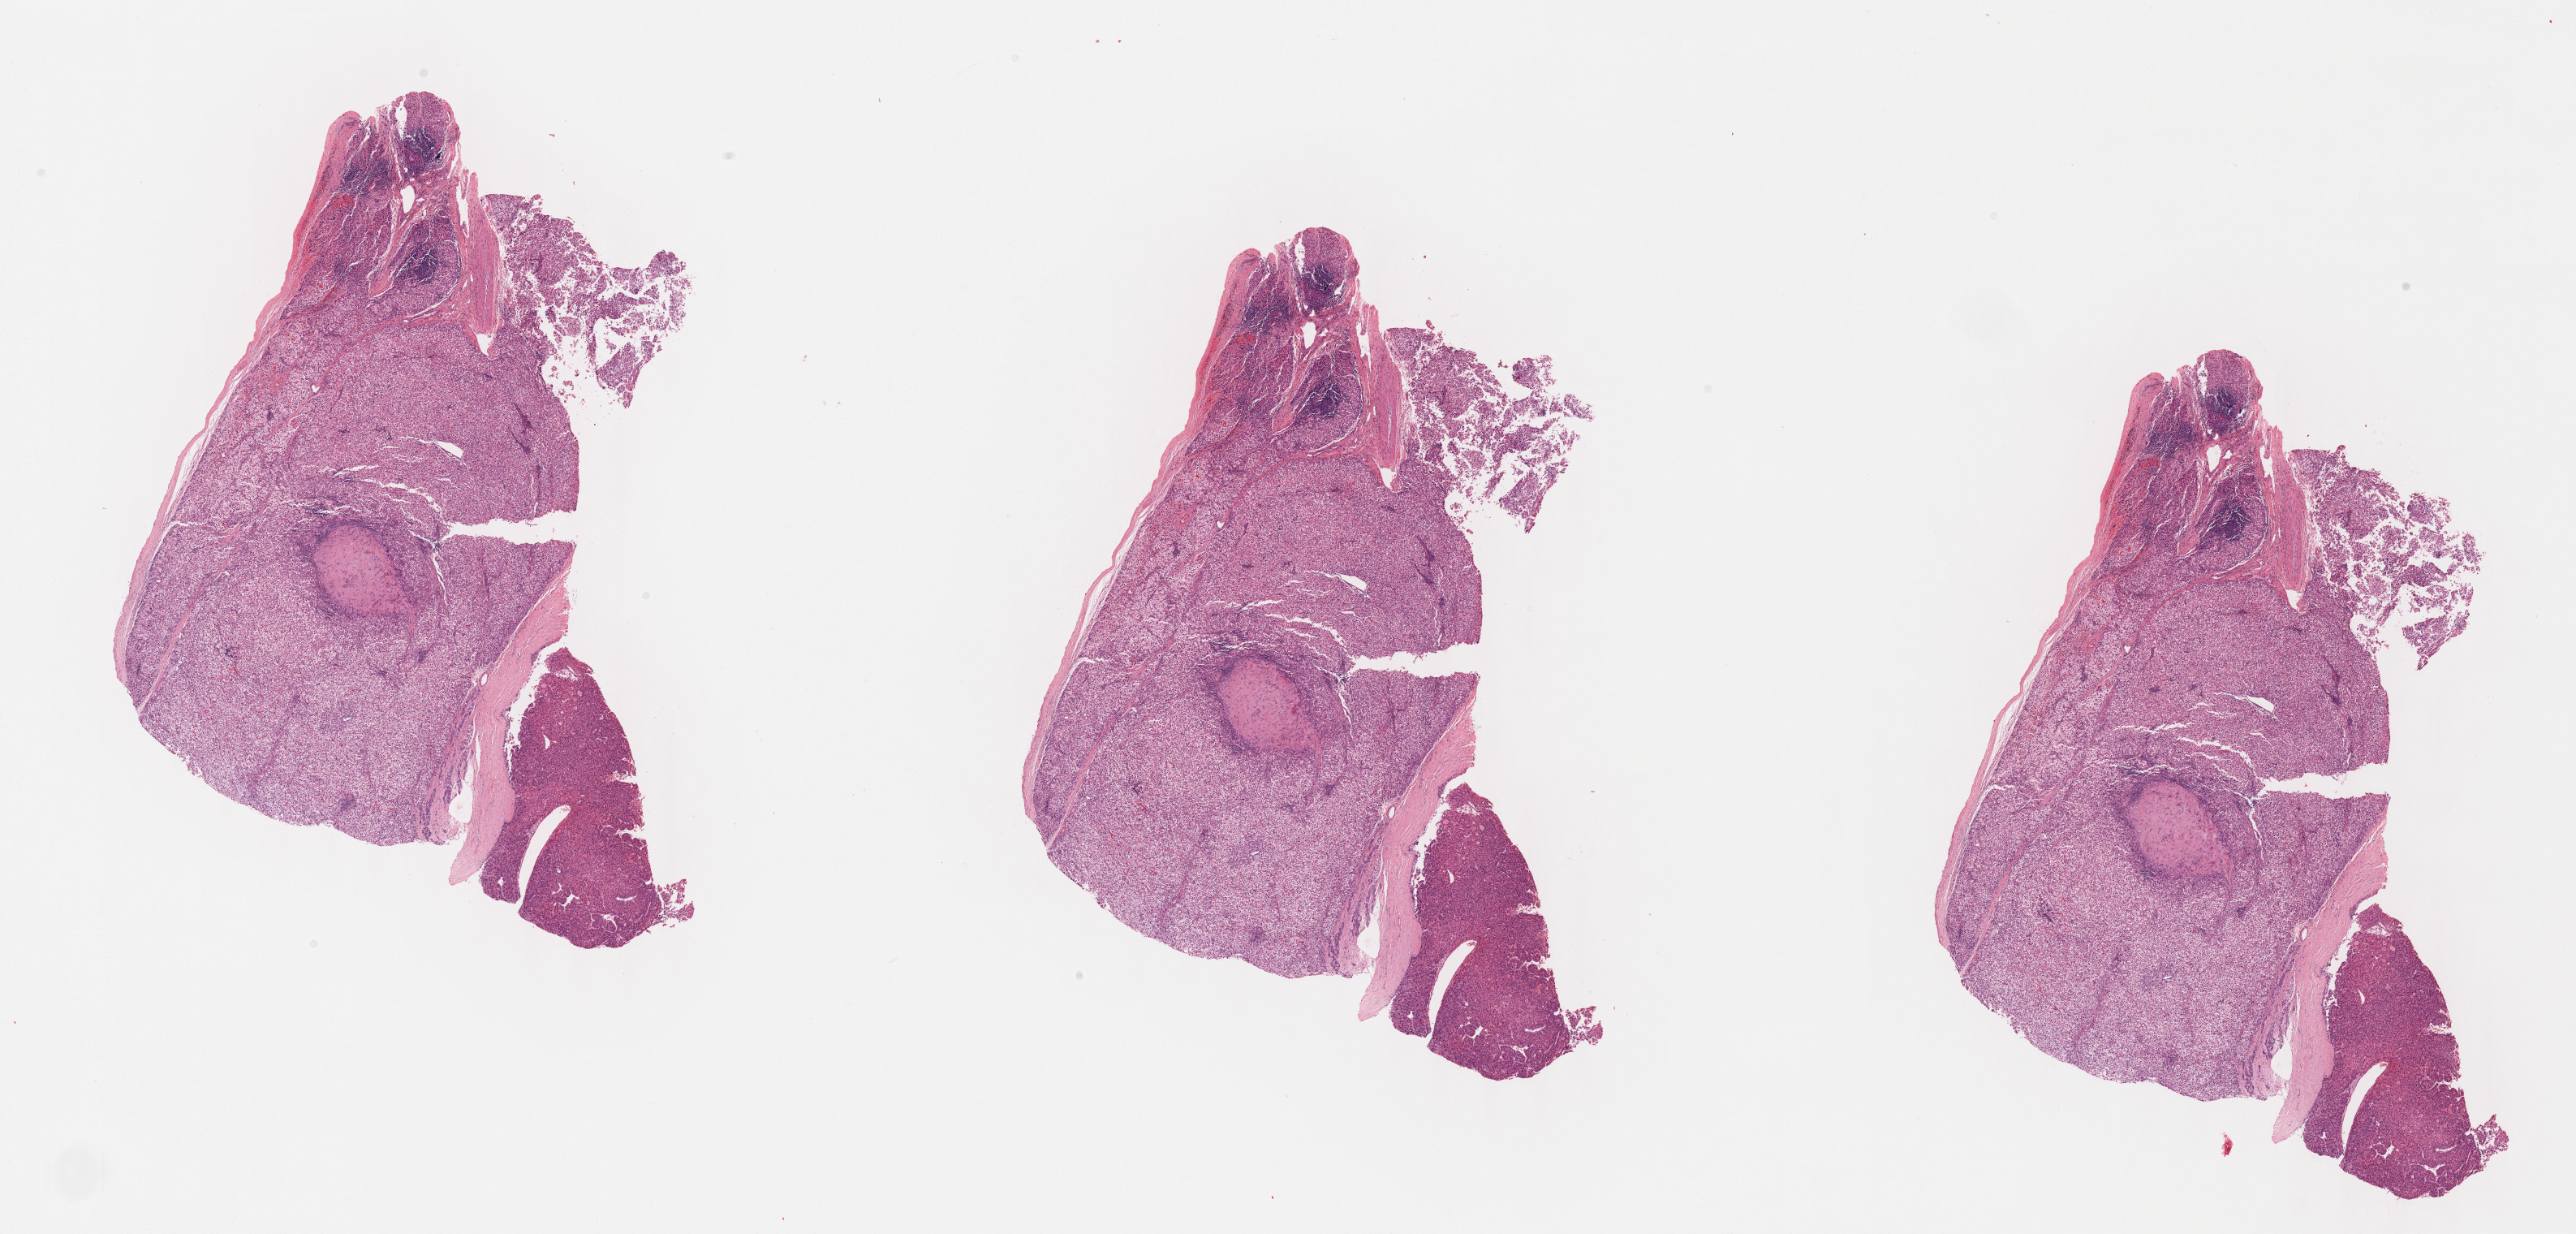
H&E whole-slide image — a low-resolution overview of the entire scanned area, about 25.7 x 12.3 mm, formalin-fixed paraffin-embedded (FFPE) diagnostic section, primary tumour sample from the liver. Male patient; age at initial diagnosis 64 years. Histologic grade: G3 (poorly differentiated).
AJCC pathologic stage: I (6th edition). TNM: T1 N0 M0. Pathologic diagnosis: Hepatocellular carcinoma, NOS.